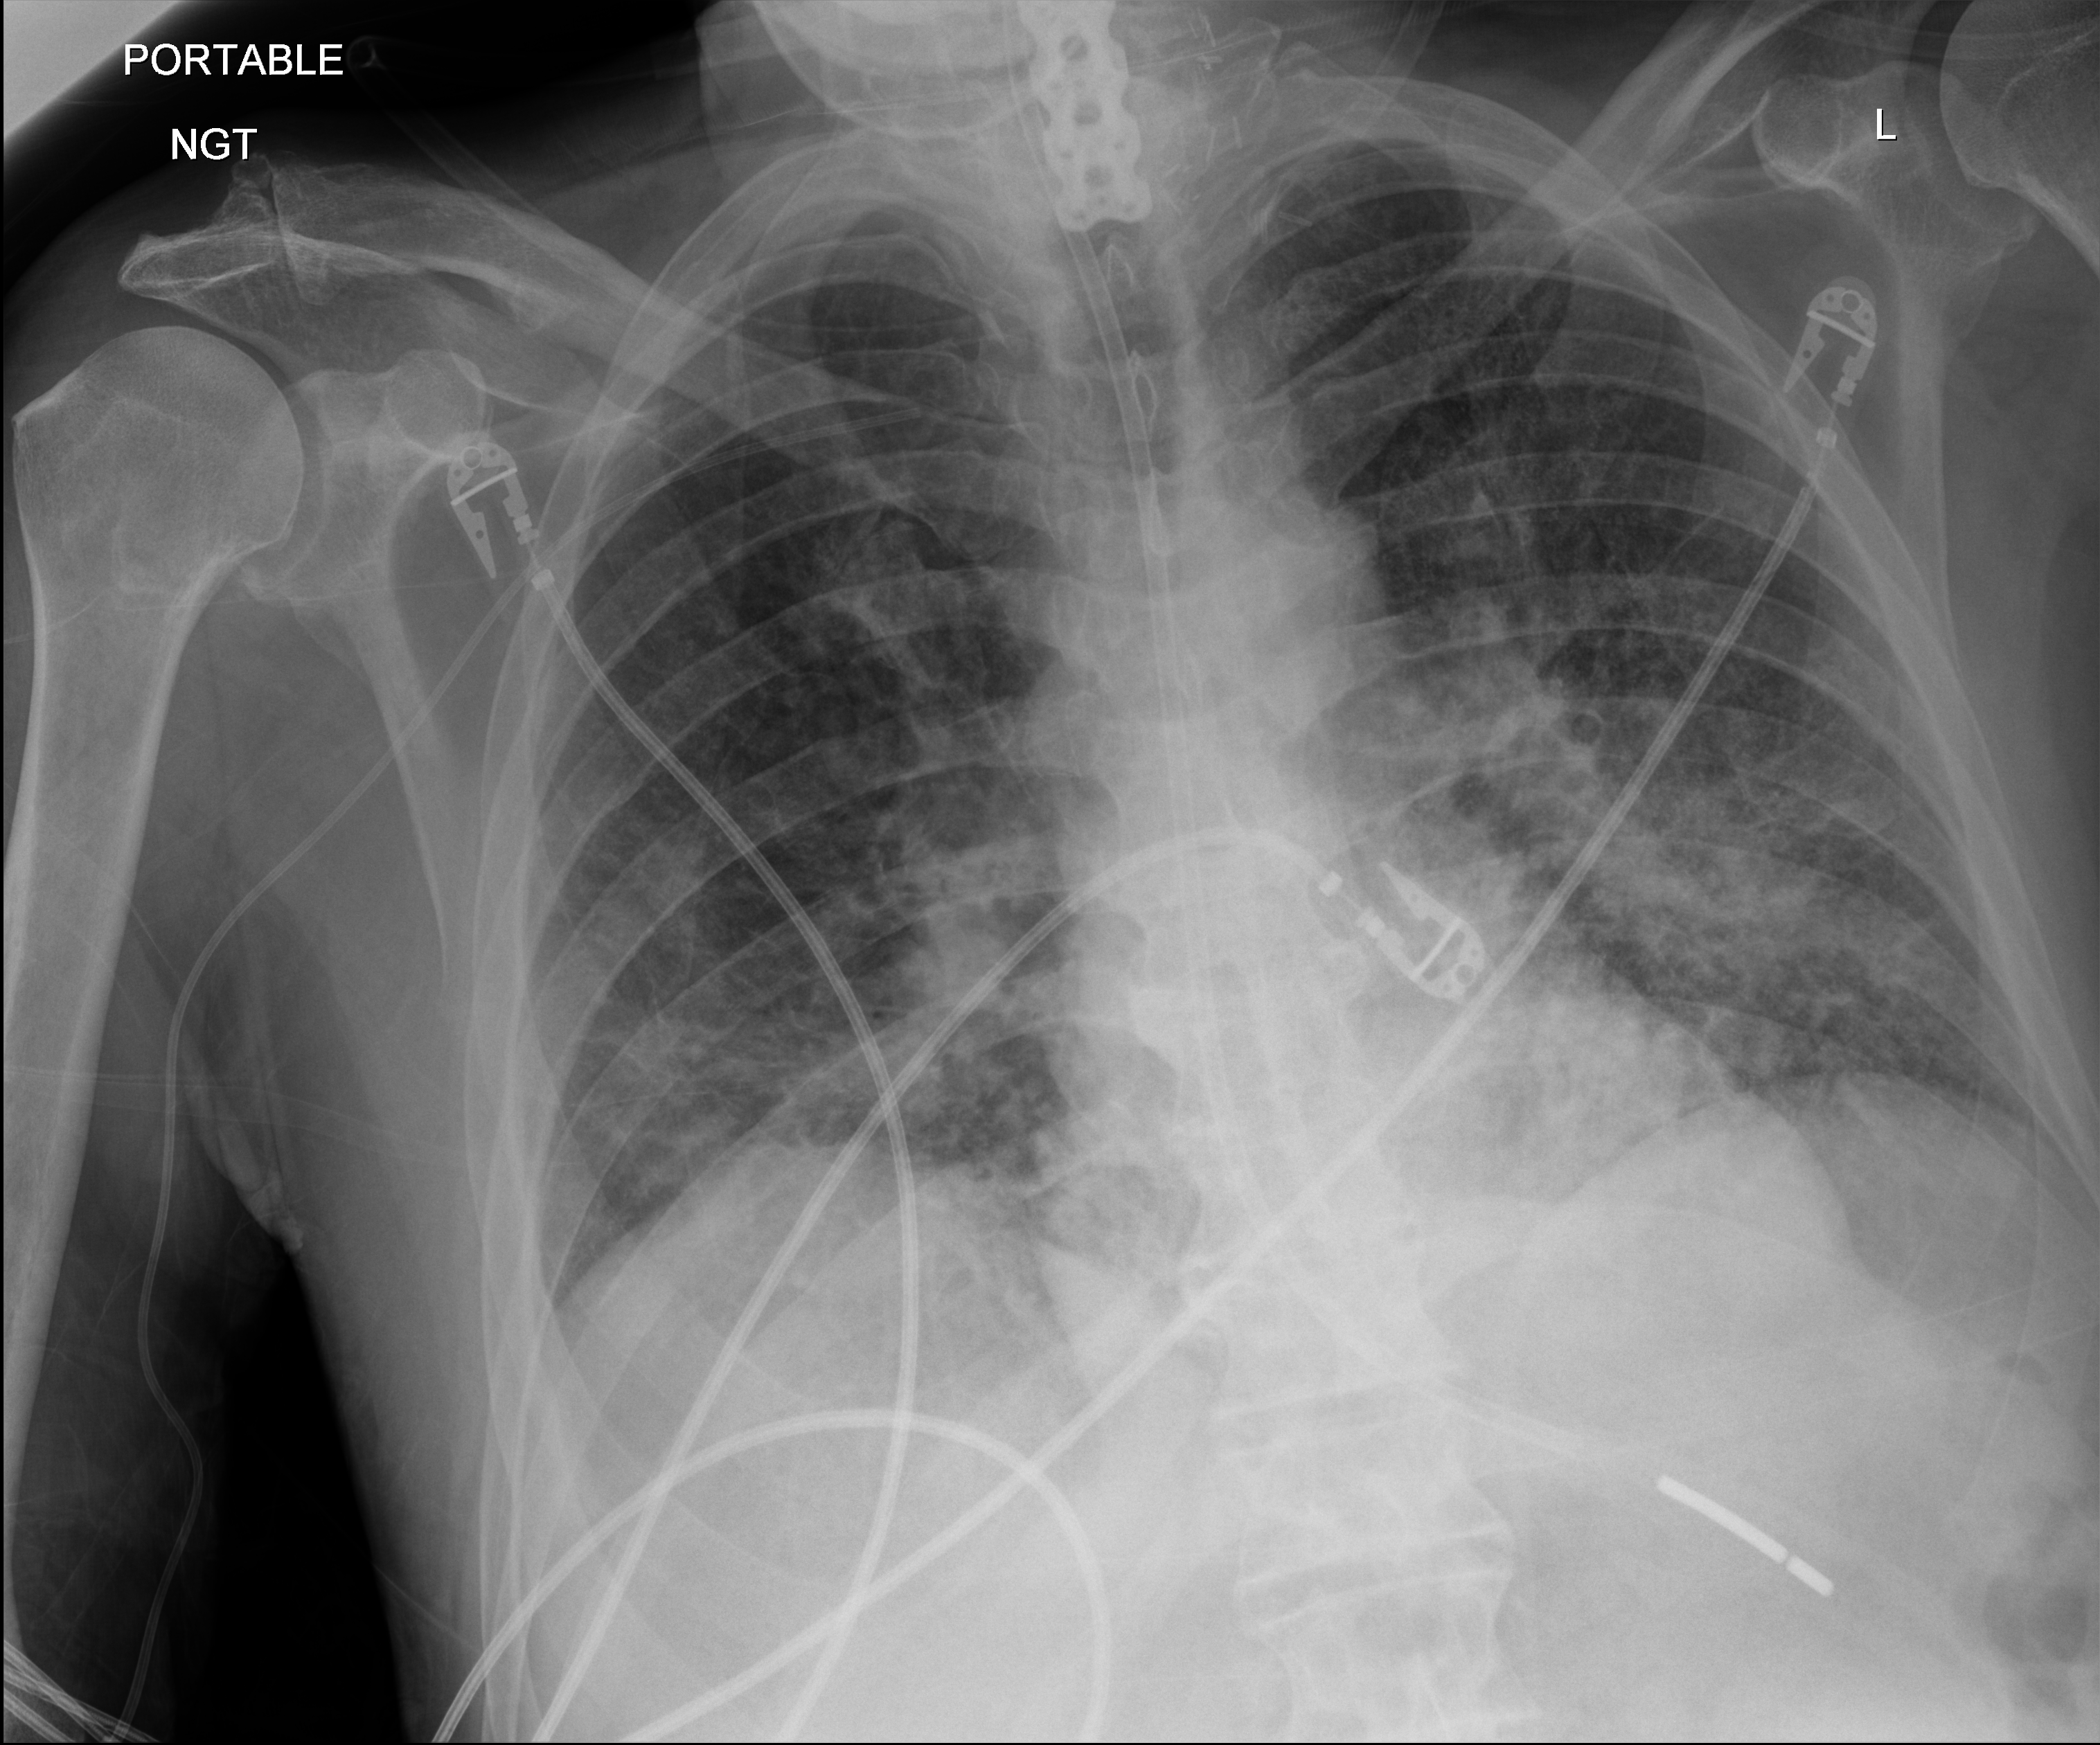
Chest X-ray (portable). Patient hospitalised with COVID-19; male, aged 60–74 years.
From the hospital-stay record, not from the radiograph (when in the stay this image was taken is not recorded):
- admitted to intensive care during this hospital stay: yes